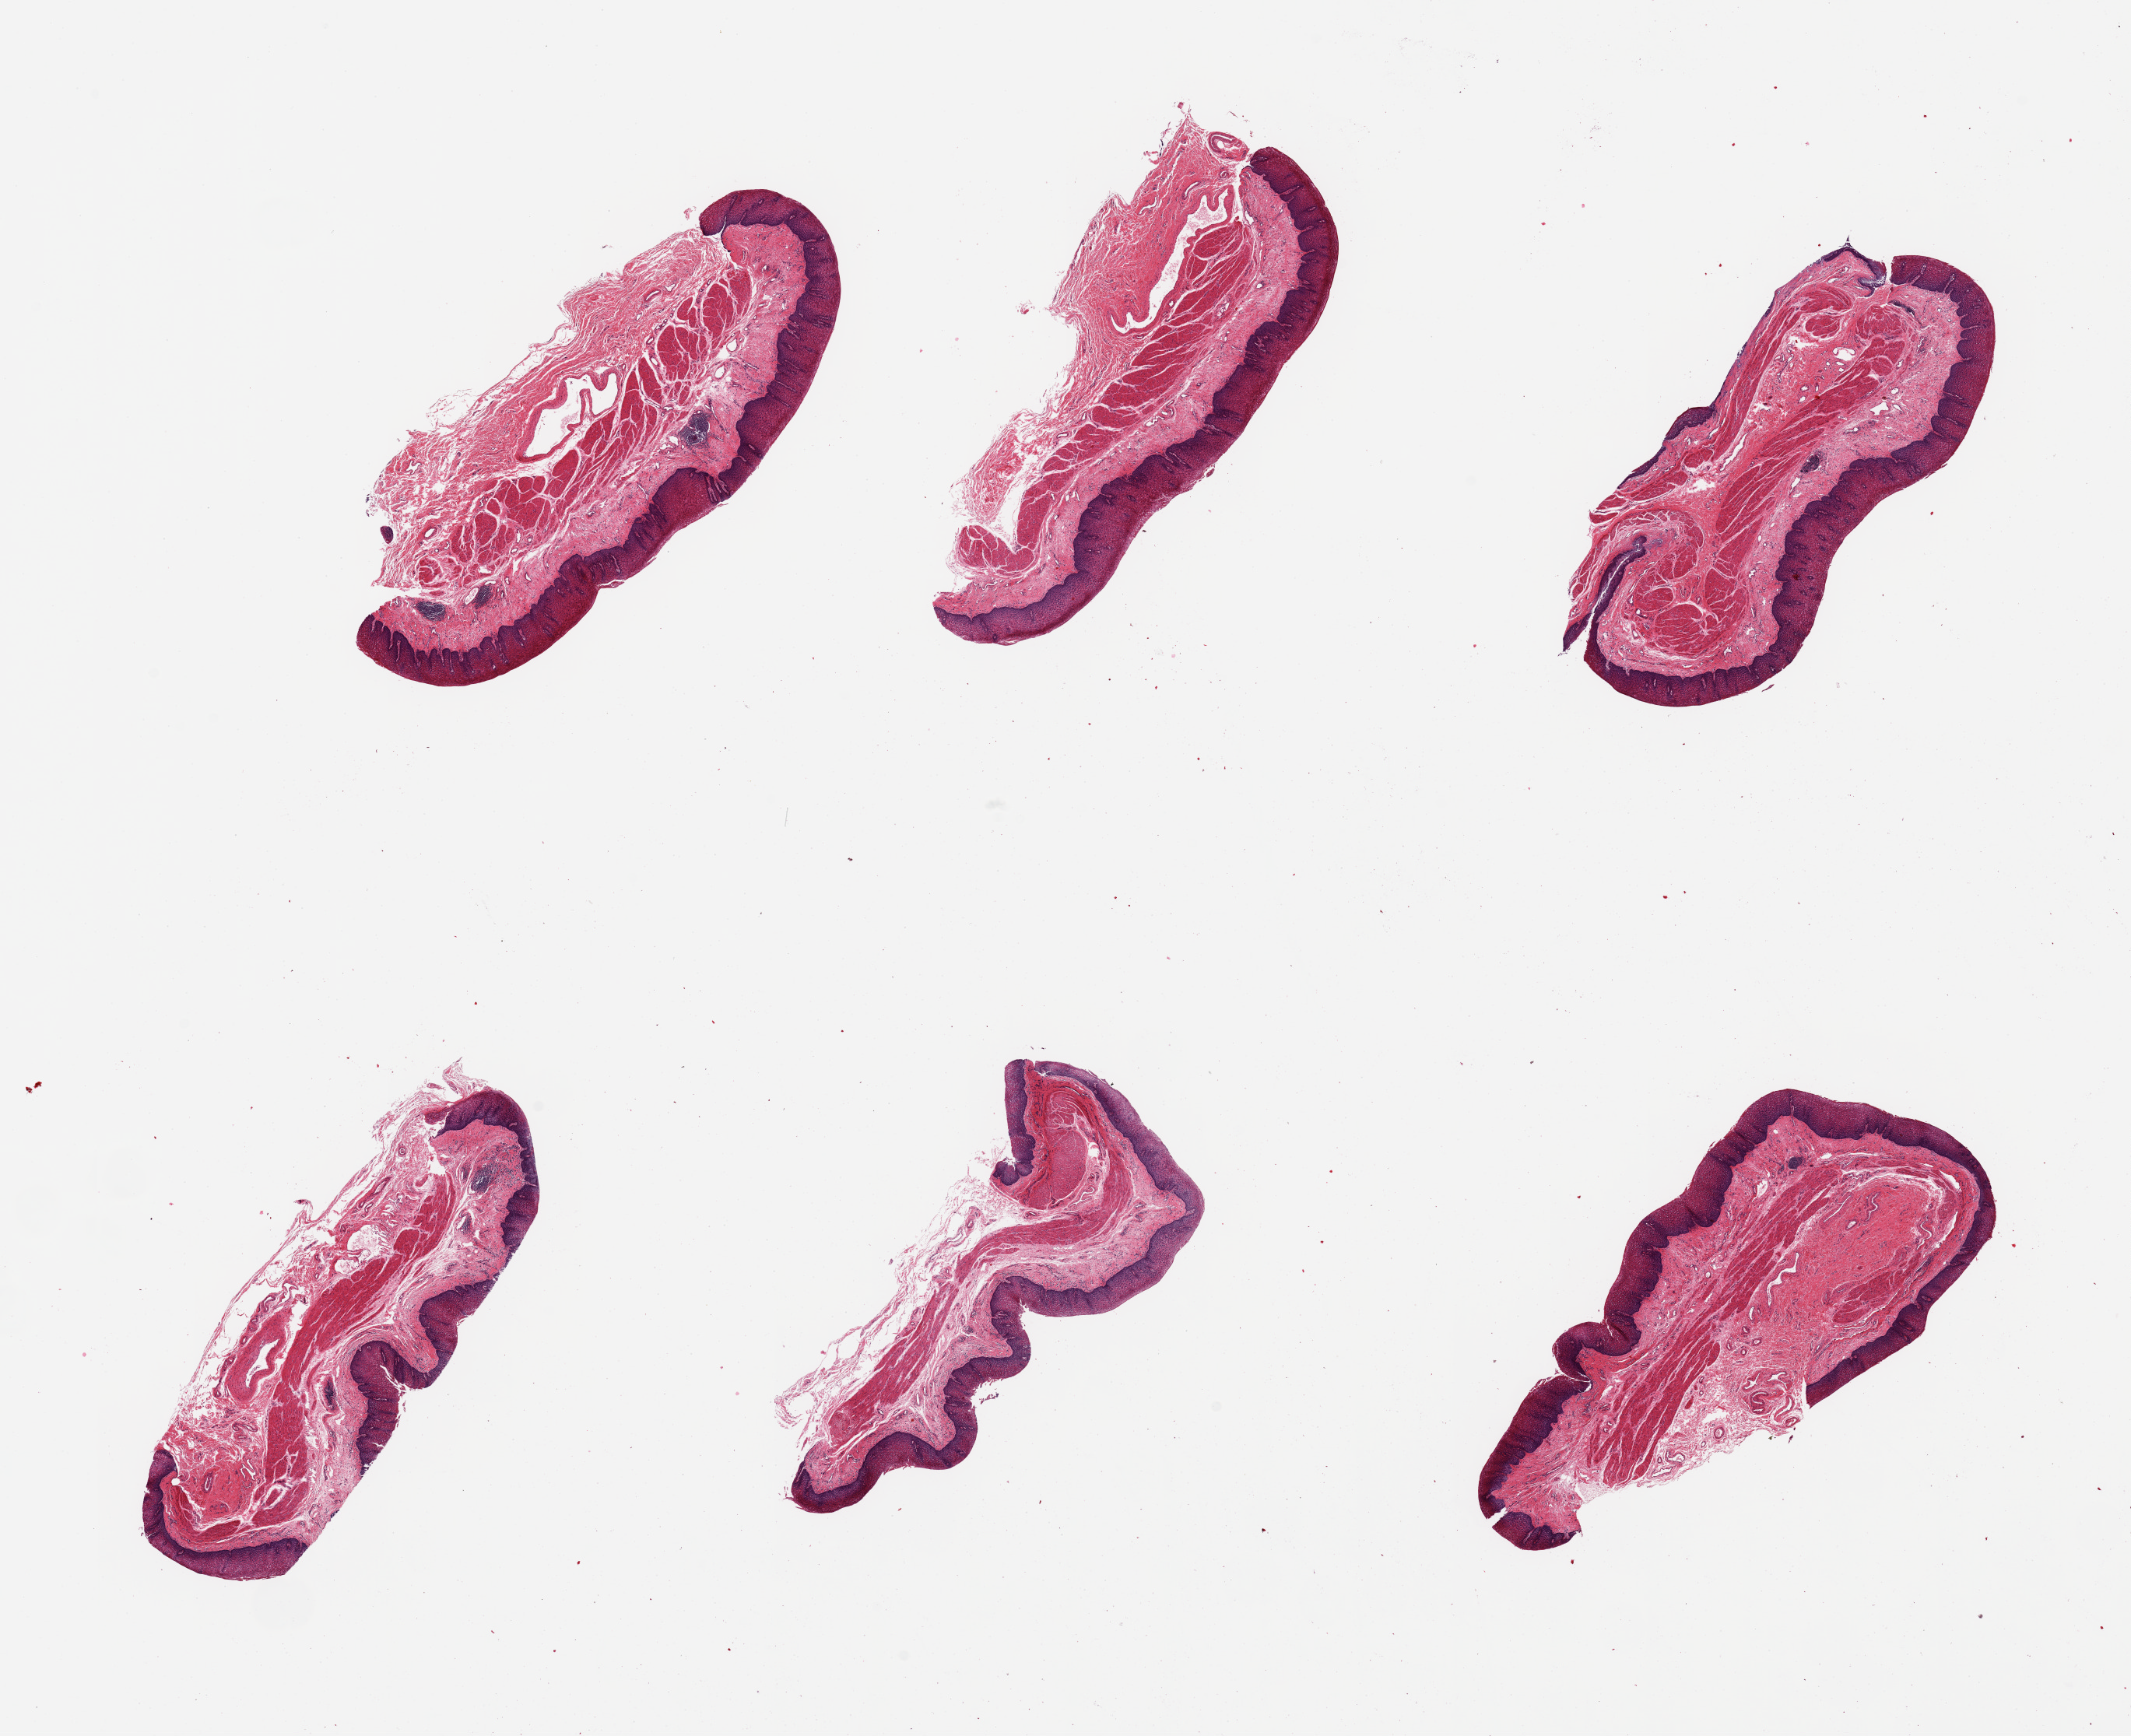
Haematoxylin and eosin whole-slide image — a low-resolution overview of the entire scanned area, about 21.7 x 17.6 mm, PAXgene-fixed paraffin-embedded (PFPE) section, section of esophageal mucous membrane (target tissue), donor tissue sample.
- pathologist's review note for this sample: 6 pieces, squamous mucosa is ~0.5mm, ~15/20% thickness